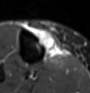
MRI of an extremity soft-tissue mass, one axial slice. Position 24 of 60 along the scan axis. STIR. MR volume resampled by the dataset authors to the PET/CT grid (not the native acquisition matrix). 3.27 mm slice thickness. 90 × 93 image matrix, field of view 88 × 91 mm. Female patient. From the clinical record (not read from this slice): histological type: undifferentiated – high grade; grade: high; site of the primary tumour: right thigh.
Structures marked on this image (expert contour drawn on MRI and transferred to this co-registered scan by the dataset authors):
- gross tumour volume (mass): bounding box [x1, y1, x2, y2] px = [33, 28, 61, 59]